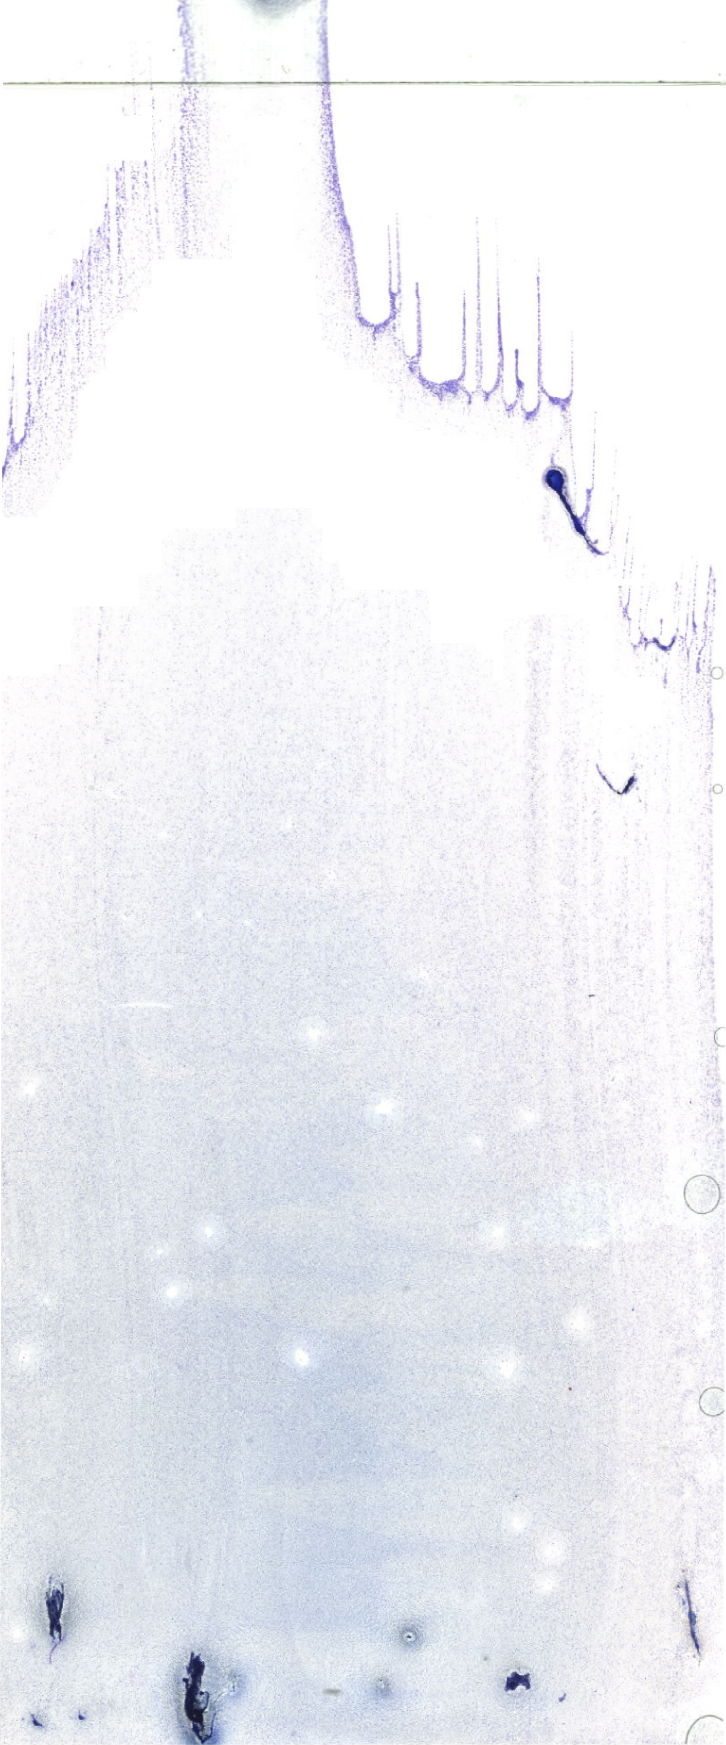
May-Grünwald-Giemsa (MGG)-stained marrow aspirate smear (whole slide) — whole scanned area (about 20.6 x 49.5 mm) shown as a low-resolution overview. Patient sex: male.
Diagnosis: Acute Monocytic Leukemia.